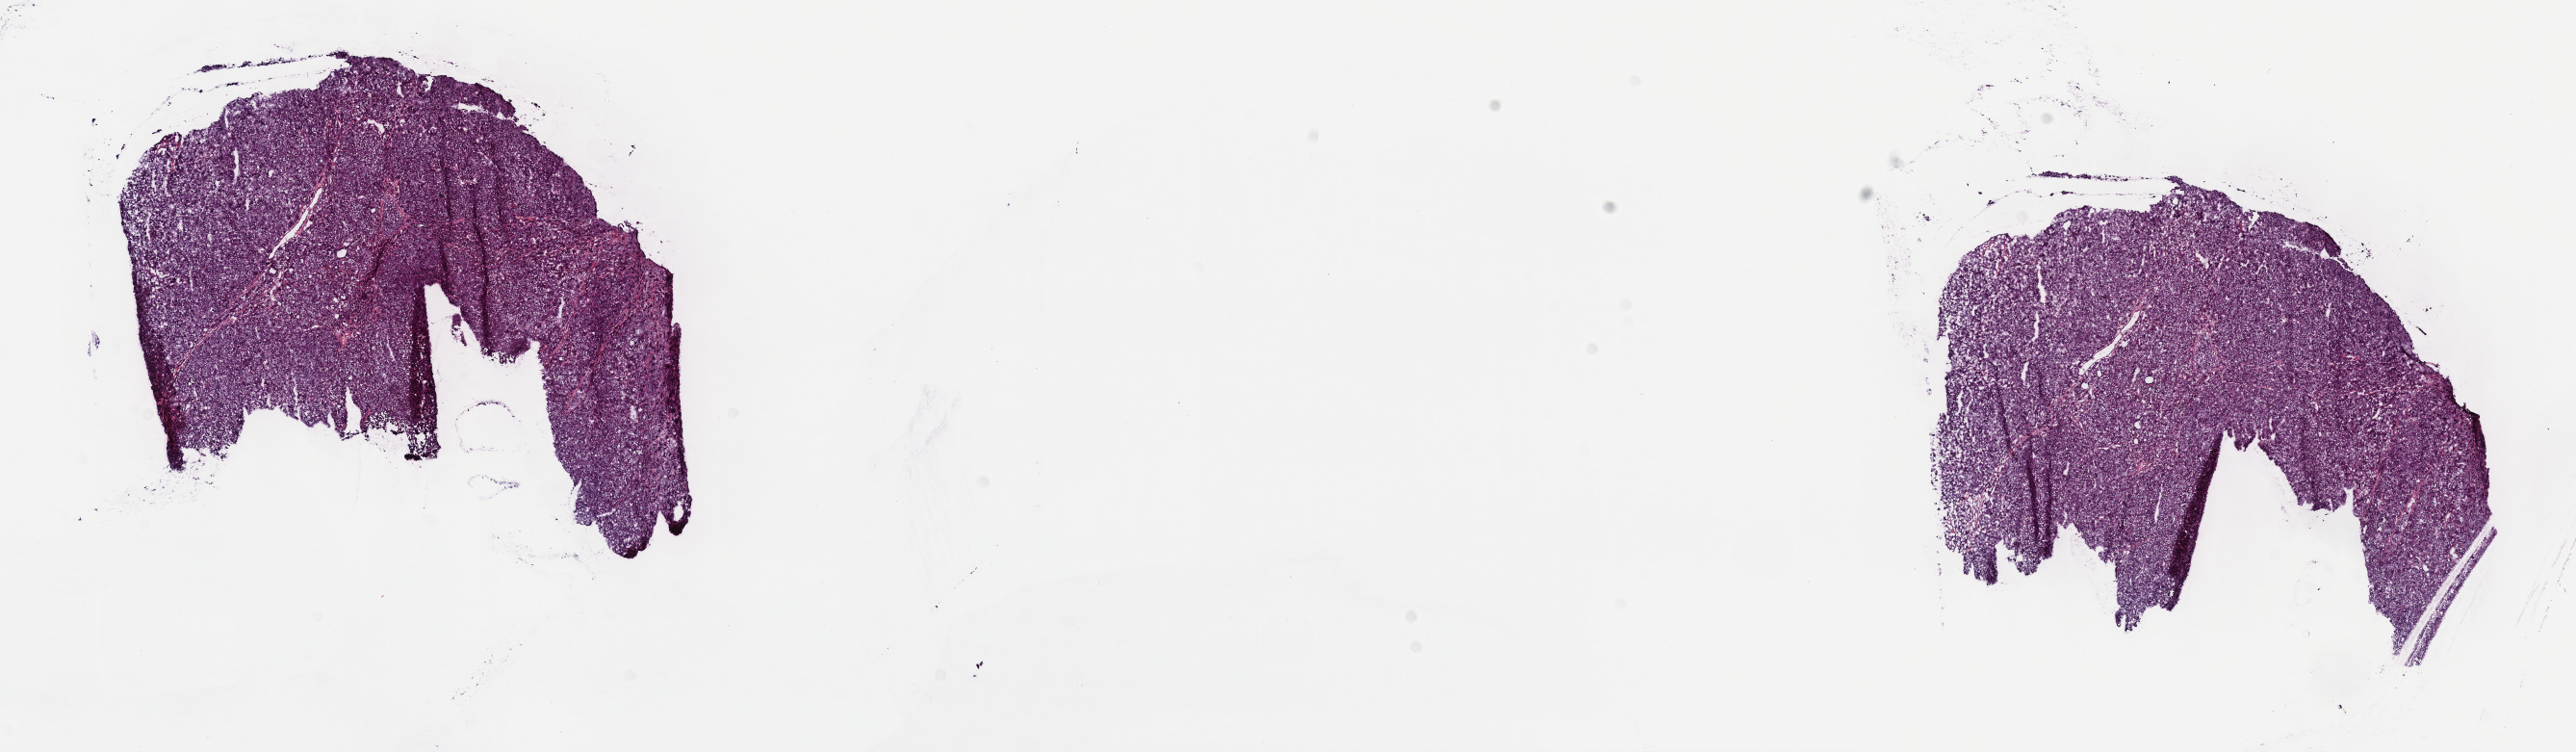
H&E-stained whole-slide image, shown as a low-resolution overview of the whole scanned area (about 21.6 x 6.3 mm); frozen section from the top of the tissue portion; primary tumour sample from the liver. Patient: male, age at initial diagnosis 62 years. Histologic grade: G3 (poorly differentiated). Slide review estimates, as recorded: tumour cells 93%, tumour nuclei 93%, normal cells 0%, stromal cells 5%, necrosis 2%. Inflammatory infiltration, as recorded: lymphocyte infiltration 4%, monocyte infiltration 2%, neutrophil infiltration 0%.
Histologic diagnosis: Hepatocellular carcinoma, NOS. AJCC pathologic stage: I (6th edition). TNM: T1 N0 M0.